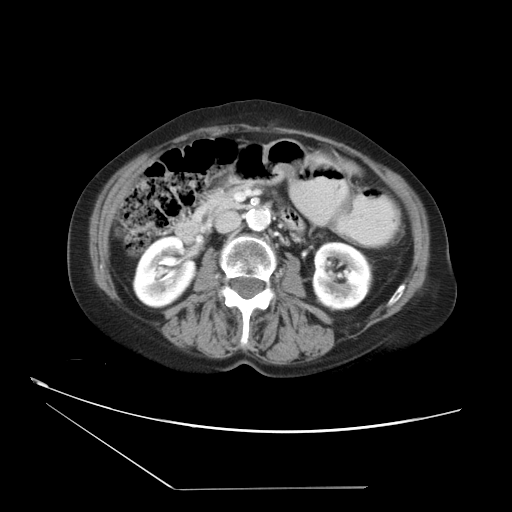
Contrast-enhanced abdominal CT, one axial slice. Slice 10 of 36 in the series (ordered by position). Soft-tissue window (W 400 / L 40 HU). 512 × 512 image matrix, field of view 384 × 384 mm. Female patient, age 81 years. Case-level facts recorded for this patient, not image findings: diagnosis: colorectal cancer liver metastases, imaged before liver resection; multiple liver metastases: no.
Annotated regions visible in this slice (expert manual segmentation):
- liver: bounding box (x1, y1, x2, y2) in pixels: (318, 157, 344, 165)